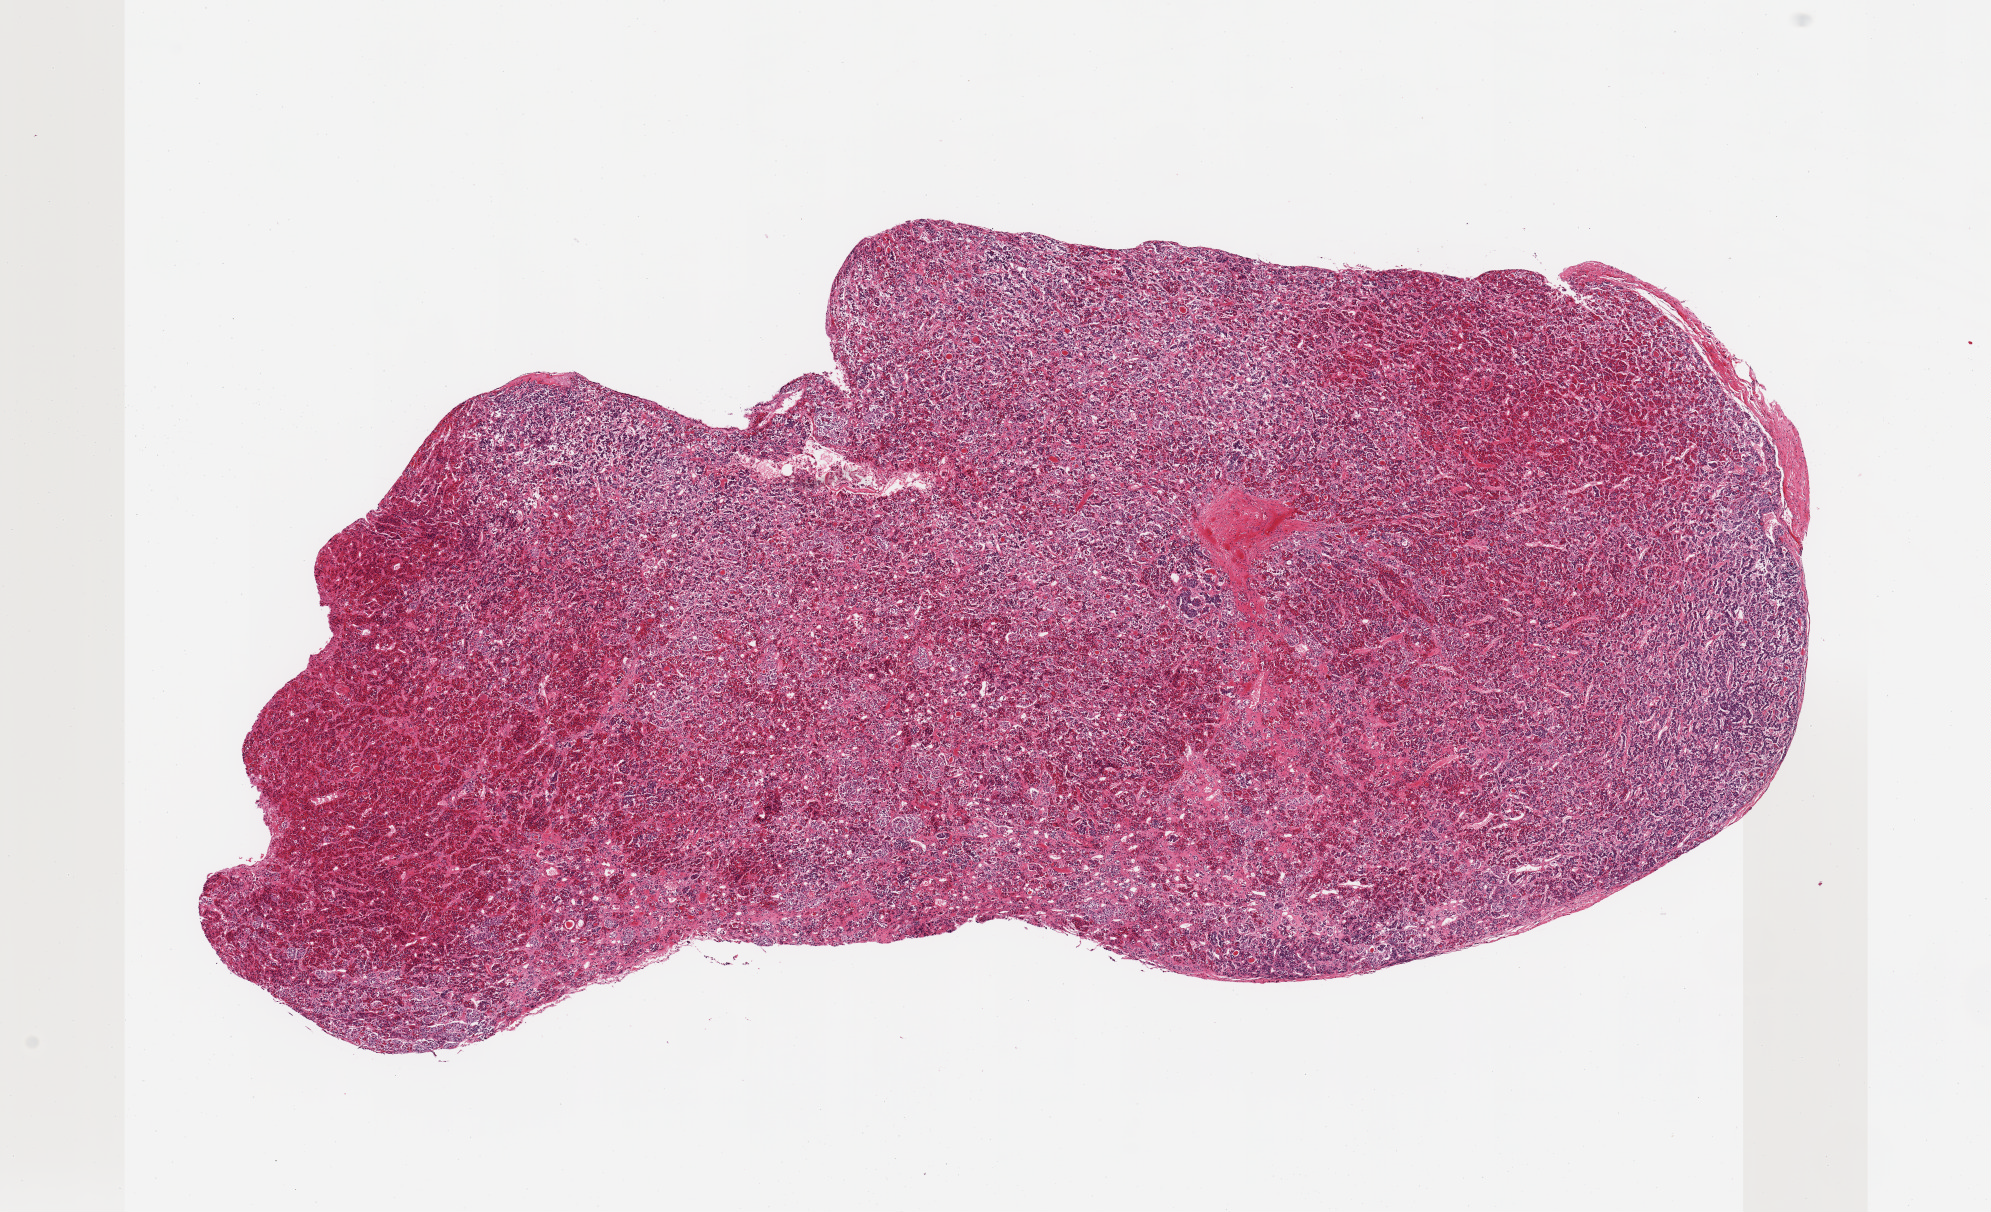
Haematoxylin and eosin whole-slide image — low-resolution overview of the scanned area, about 15.8 x 9.6 mm (from a 20x scan). PAXgene-fixed, paraffin-embedded tissue. Section of pituitary (target tissue). Tissue donor sample. Donor sex: female.
Pathologist's review note for this sample: 1 piece, adenohypophysis.